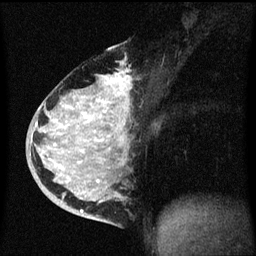
Breast MRI (dynamic contrast-enhanced), one sagittal slice; slice 34 of 60 in the series (ordered by position); dynamic contrast-enhanced series, image 2 of 3 at this slice position (ordered by acquisition); 1.5 T; TE 4.2 ms, TR 8.4 ms; 256 × 256 image matrix. Patient: female, 34 years. From the clinical record (not read from this slice): setting: breast cancer imaged before/during neoadjuvant chemotherapy; receptor status: HR-positive, HER2-negative.
Outlined on this slice (semi-automatic segmentation, software-assisted and operator-edited):
- analysis volume of interest (the breast-tissue region the enhancement analysis was run in; not a lesion): bounding box (x1, y1, x2, y2) in pixels: (34, 48, 135, 215)
- tumour enhancement mask (voxels above the 70 % enhancement threshold inside the analysis volume of interest): (36, 78, 125, 213)